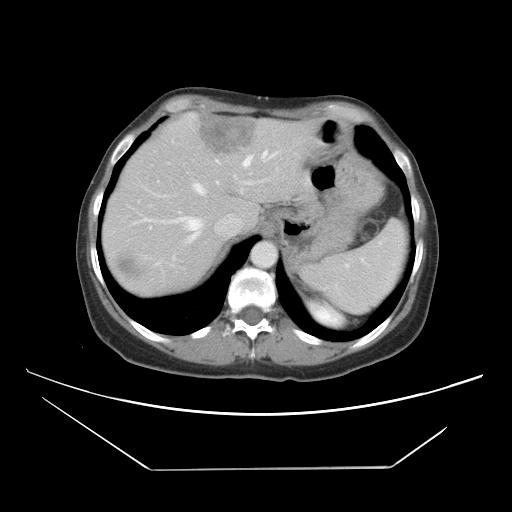
Contrast-enhanced abdominal CT, one axial slice. Slice 33 of 42 in the series (ordered by position). 120 kVp. Soft-tissue window (W 400 / L 40 HU). 5 mm slice thickness. 512 × 512 image matrix, field of view 399 × 399 mm. Female patient, age 52 years. Case-level facts recorded for this patient, not image findings: diagnosis: colorectal cancer liver metastases, imaged before liver resection; multiple liver metastases: yes; largest metastasis: 5.5 cm.
Outlined on this slice (expert manual segmentation):
- hepatic veins: box from (x=133, y=150) to (x=277, y=264) px
- liver: (x=105, y=115)–(x=317, y=294)
- planned liver remnant (the part of the liver to remain after resection): (x=122, y=123)–(x=251, y=225)
- portal vein (with intrahepatic branches): (x=178, y=167)–(x=278, y=214)
- liver metastasis: (x=200, y=119)–(x=258, y=154)
- liver metastasis: (x=121, y=259)–(x=137, y=277)